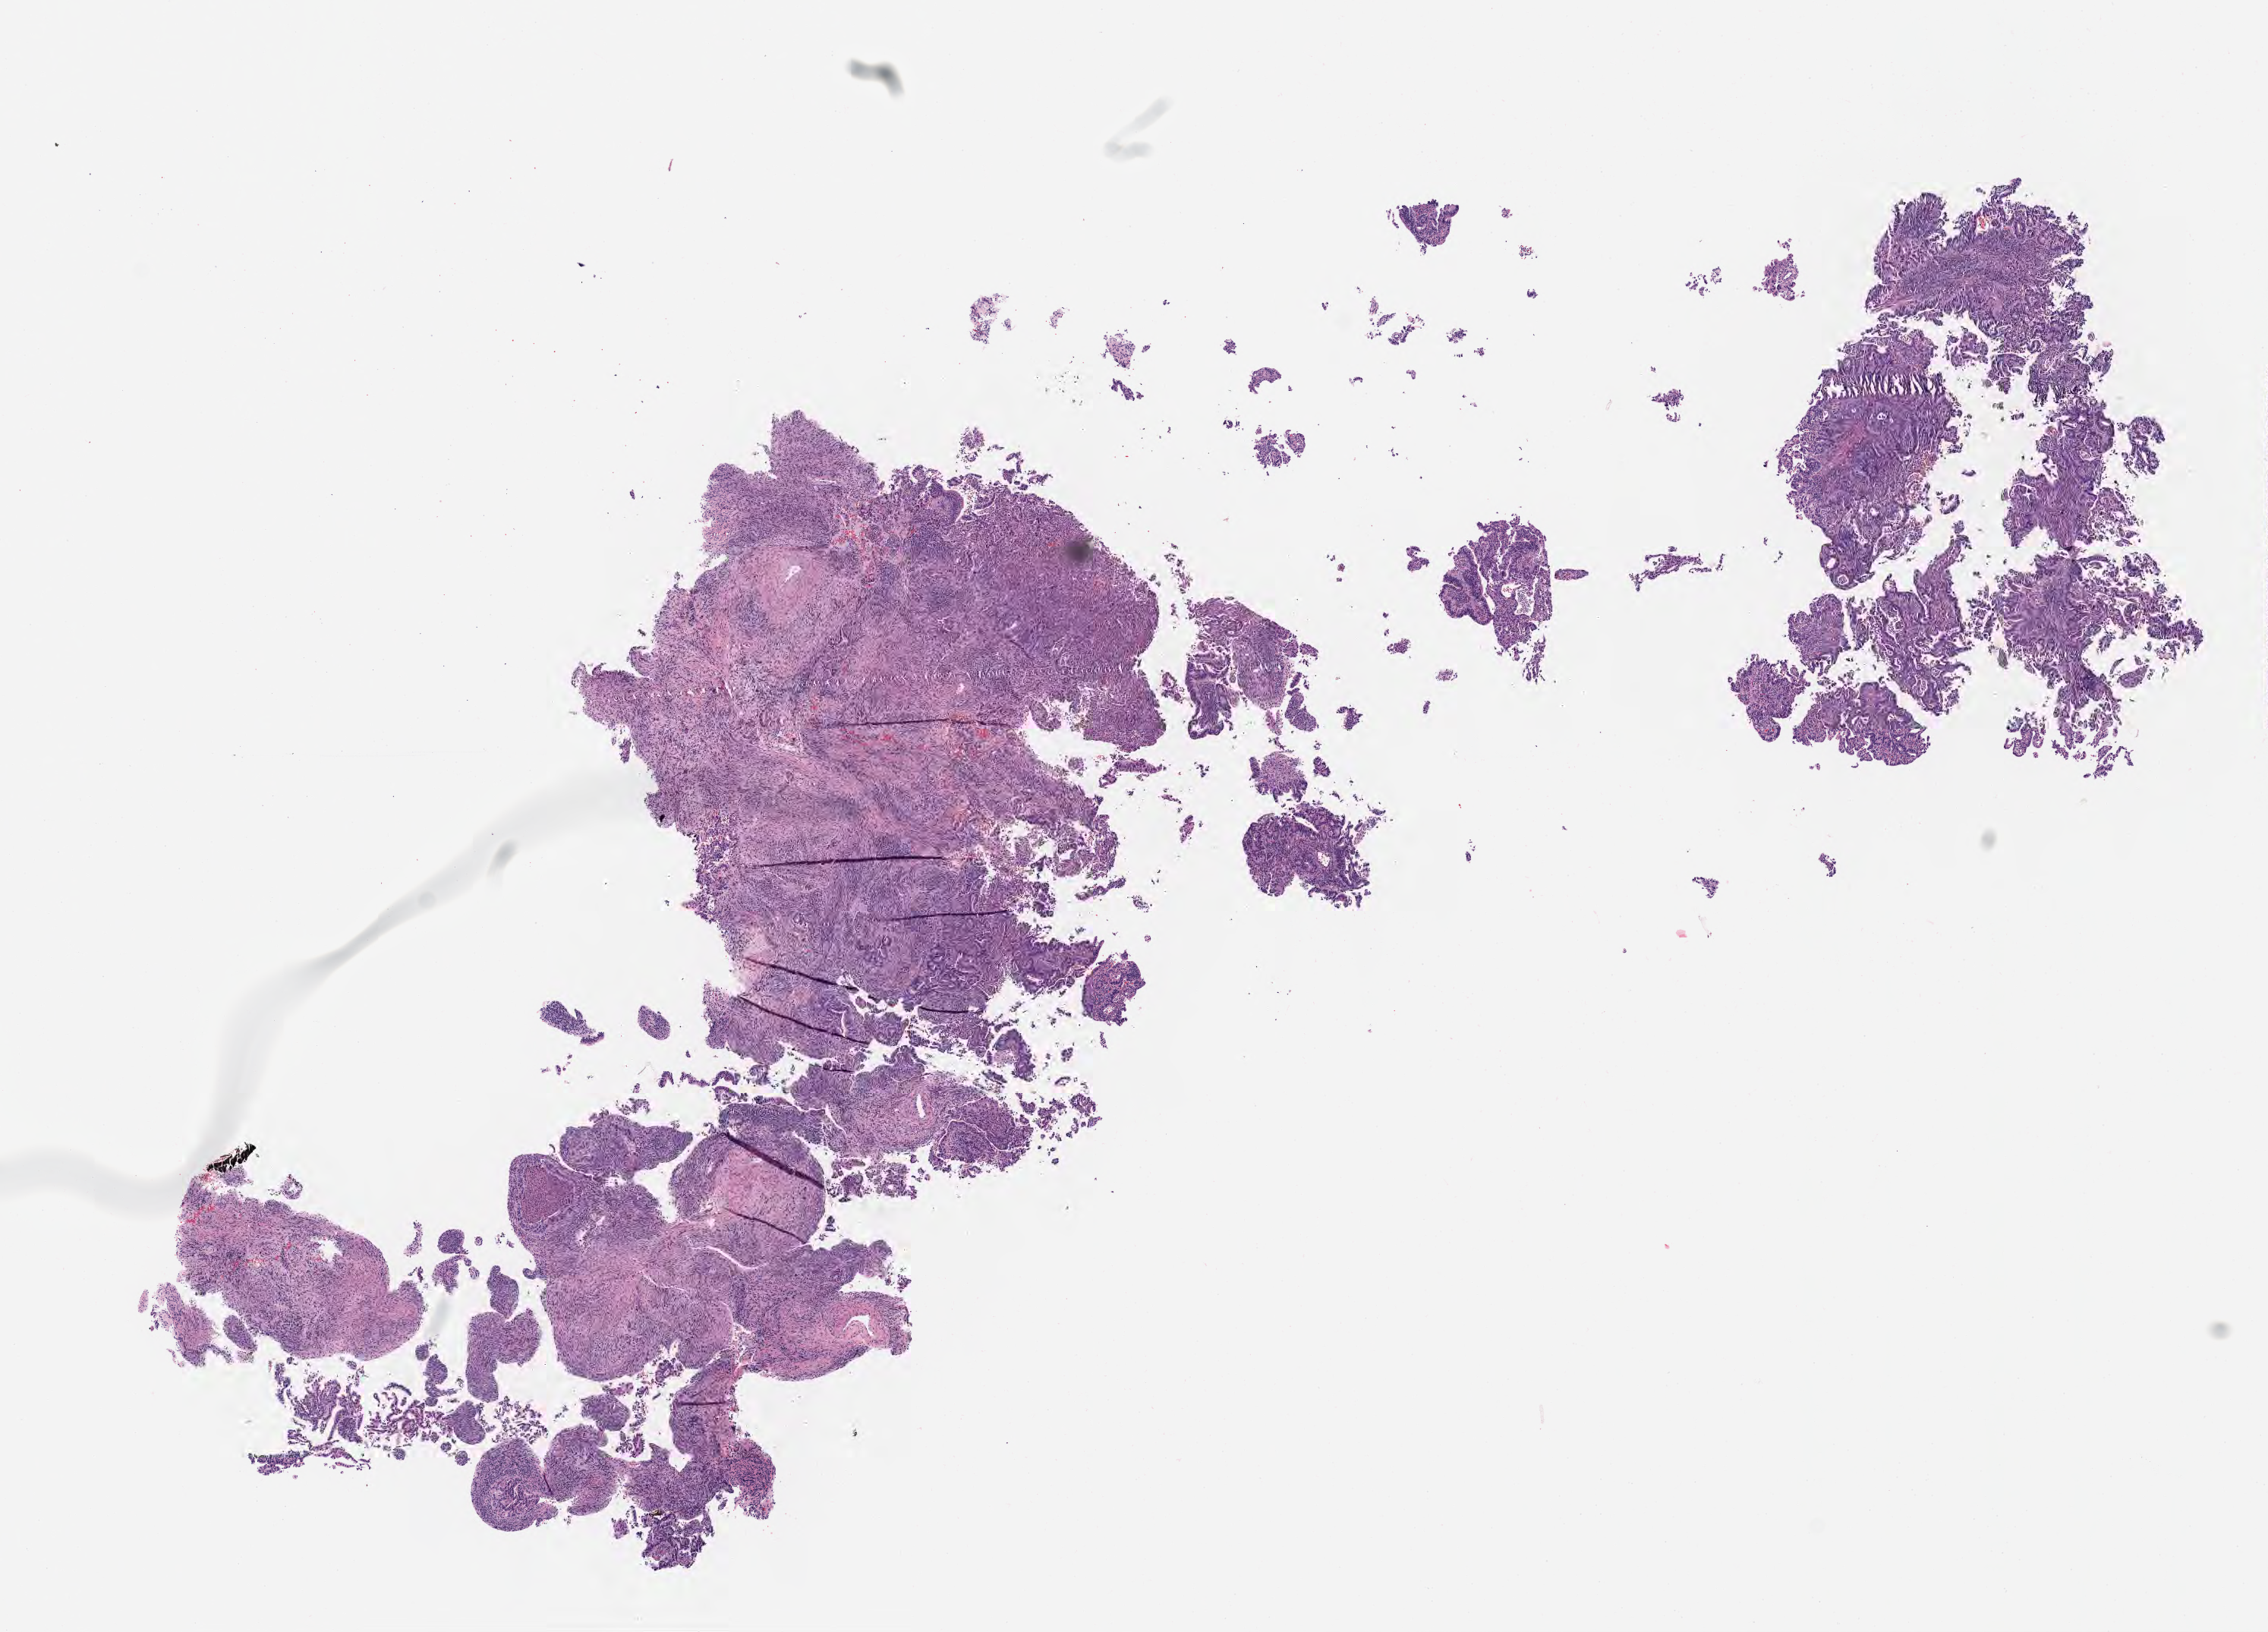
Haematoxylin and eosin whole-slide image — whole scanned area (about 12.1 x 8.7 mm) shown as a low-resolution overview. Specimen: tumor tissue. Anatomic site: cervix. Female patient, 42 years old.
Diagnosis: Adenocarcinoma, NOS.